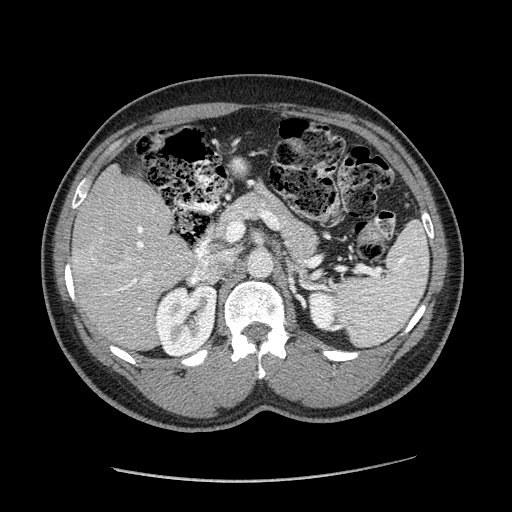
Contrast-enhanced abdominal CT (liver protocol), one axial slice; position 91 of 182 along the scan axis; reconstruction kernel STANDARD; 120 kVp; soft-tissue window (W 400 / L 40 HU); 2.5 mm slice thickness; 512 × 512 image matrix. Case-level facts recorded for this patient, not image findings: diagnosis: hepatocellular carcinoma (patient treated with transarterial chemoembolisation; whether this scan precedes or follows treatment is not stated here); TNM stage (as recorded): Stage-I; Child-Pugh class: A.
Outlined on this slice (semi-automatically segmented with operator editing):
- liver parenchyma outside the tumour (the mass and vessels are separate outlines, so this box may not span the whole liver): bounding box [x1, y1, x2, y2] px = [70, 164, 194, 350]
- mass: [90, 230, 130, 270]
- liver vessels: [75, 226, 156, 310]